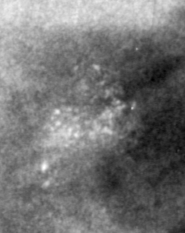
Region of interest cut from a scanned film mammogram (one marked finding); left breast; CC view.
- Calcifications, morphology pleomorphic, distribution clustered; BI-RADS assessment category 4; subtlety rating 3 on a 1 (subtle) to 5 (obvious) scale; pathology (as recorded): malignant.